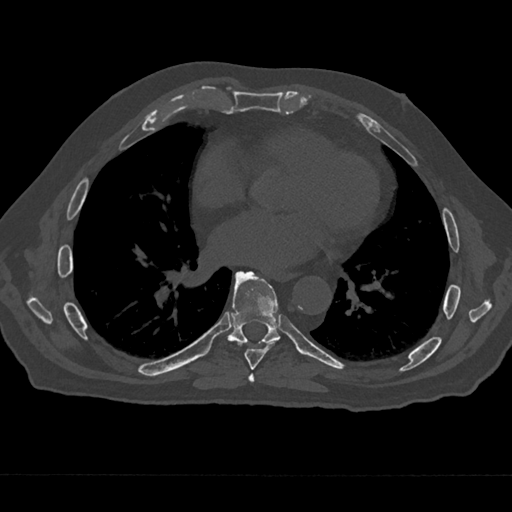
CT including the spine, one axial slice. Slice 343 of 797 in the series (ordered by position). Reconstruction kernel Br40s/3. 120 kVp. Bone window (W 1800 / L 400 HU). 0.5 mm slice thickness. 512 × 512 image matrix, field of view 377 × 377 mm. Patient: male, 75 years. From the clinical record (not read from this slice): primary cancer: renal; vertebrae with lytic lesions (as recorded): T4.
Structures marked on this image (semi-automatically segmented with operator editing):
- T6 vertebra: bounding box (x1, y1, x2, y2) in pixels: (248, 373, 255, 383)
- T7 vertebra: (237, 271, 277, 370)
- T8 vertebra: (220, 271, 280, 345)